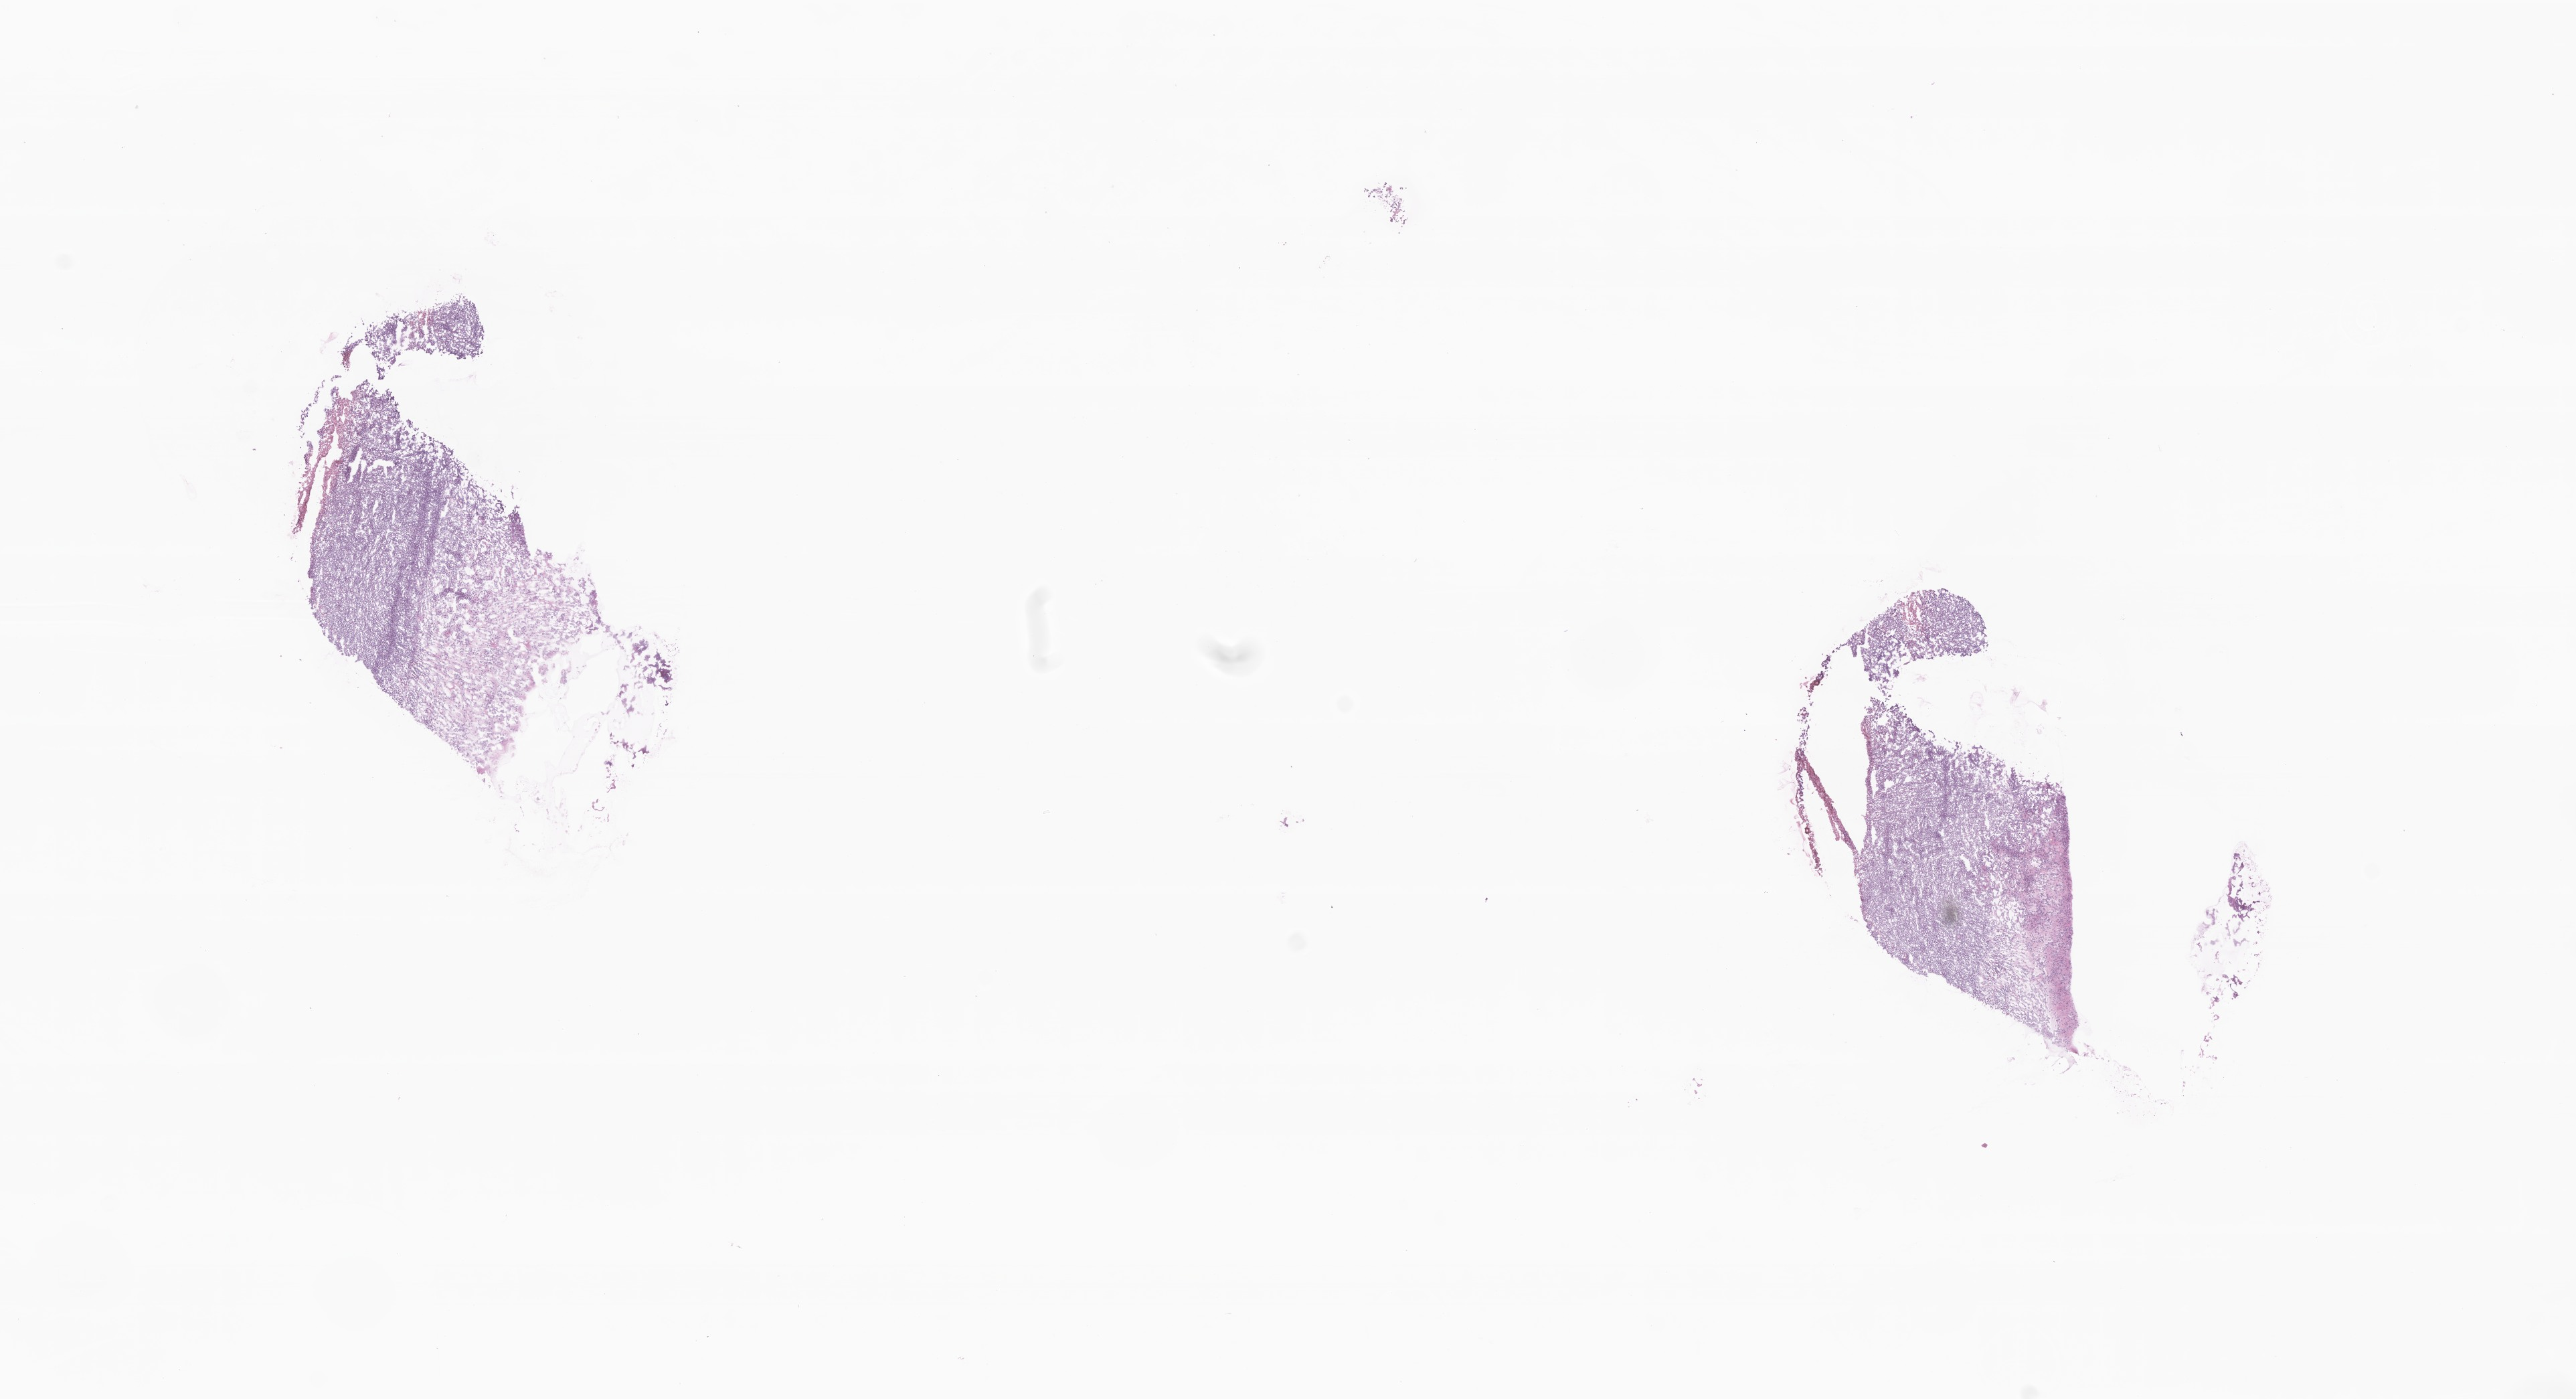
Haematoxylin and eosin whole-slide image, a low-resolution overview of the entire scanned area, about 16.2 x 8.8 mm; frozen section (tissue freezing medium); metastatic tumor tissue. Male patient; age at initial diagnosis 61 years. Slide review estimates, as recorded: tumor cells 75%, tumor nuclei 75%, stromal cells 21%, necrosis 4%, normal cells 0%. Inflammatory infiltration, as recorded: lymphocyte infiltration 5%, monocyte infiltration 3%, neutrophil infiltration 8%.
Section: bottom of the tissue portion. Patient diagnosis (primary): Malignant melanoma, NOS.